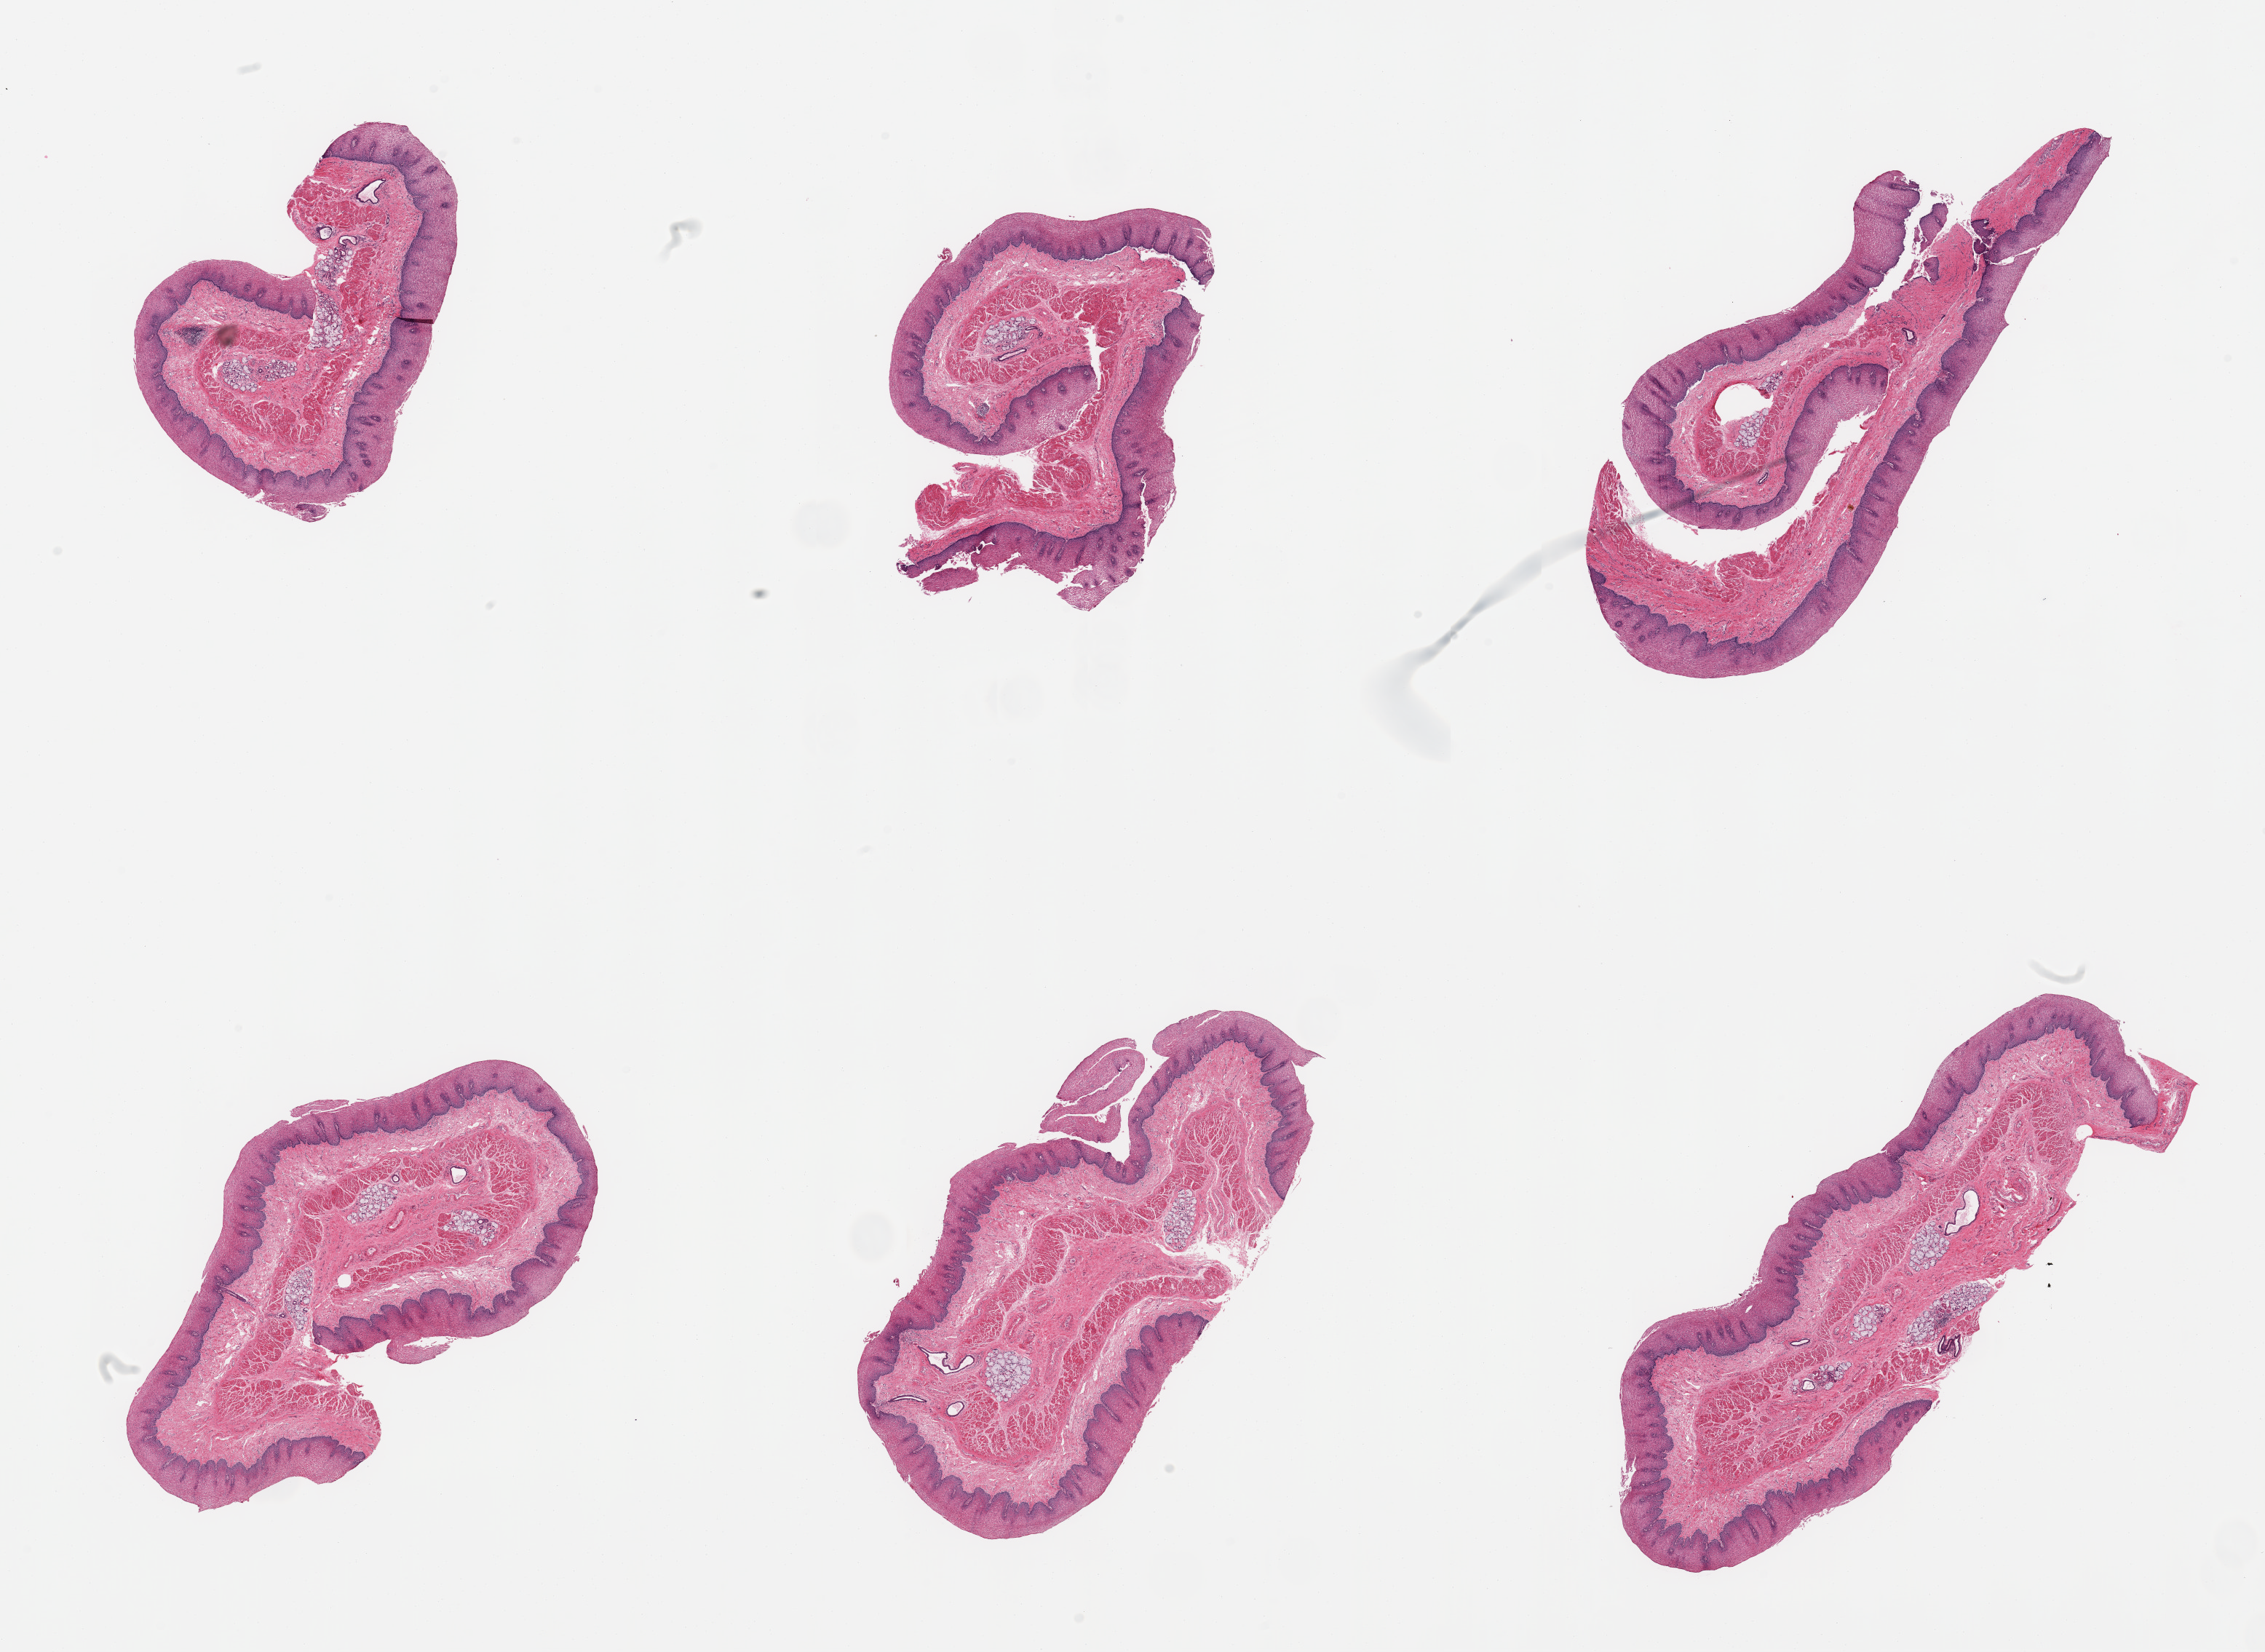
Digitized hematoxylin and eosin (H&E)-stained section — low-resolution overview of the scanned area, about 24.6 x 18.0 mm; PAXgene-fixed, paraffin-embedded tissue; sampled site (target tissue): esophageal mucous membrane; donor tissue sample. Donor sex: male.
Review note (as recorded): 6 pieces, squamous mucosa up to ~0.5mm, ~30-40% thickness; Submucosal mucus glands present.